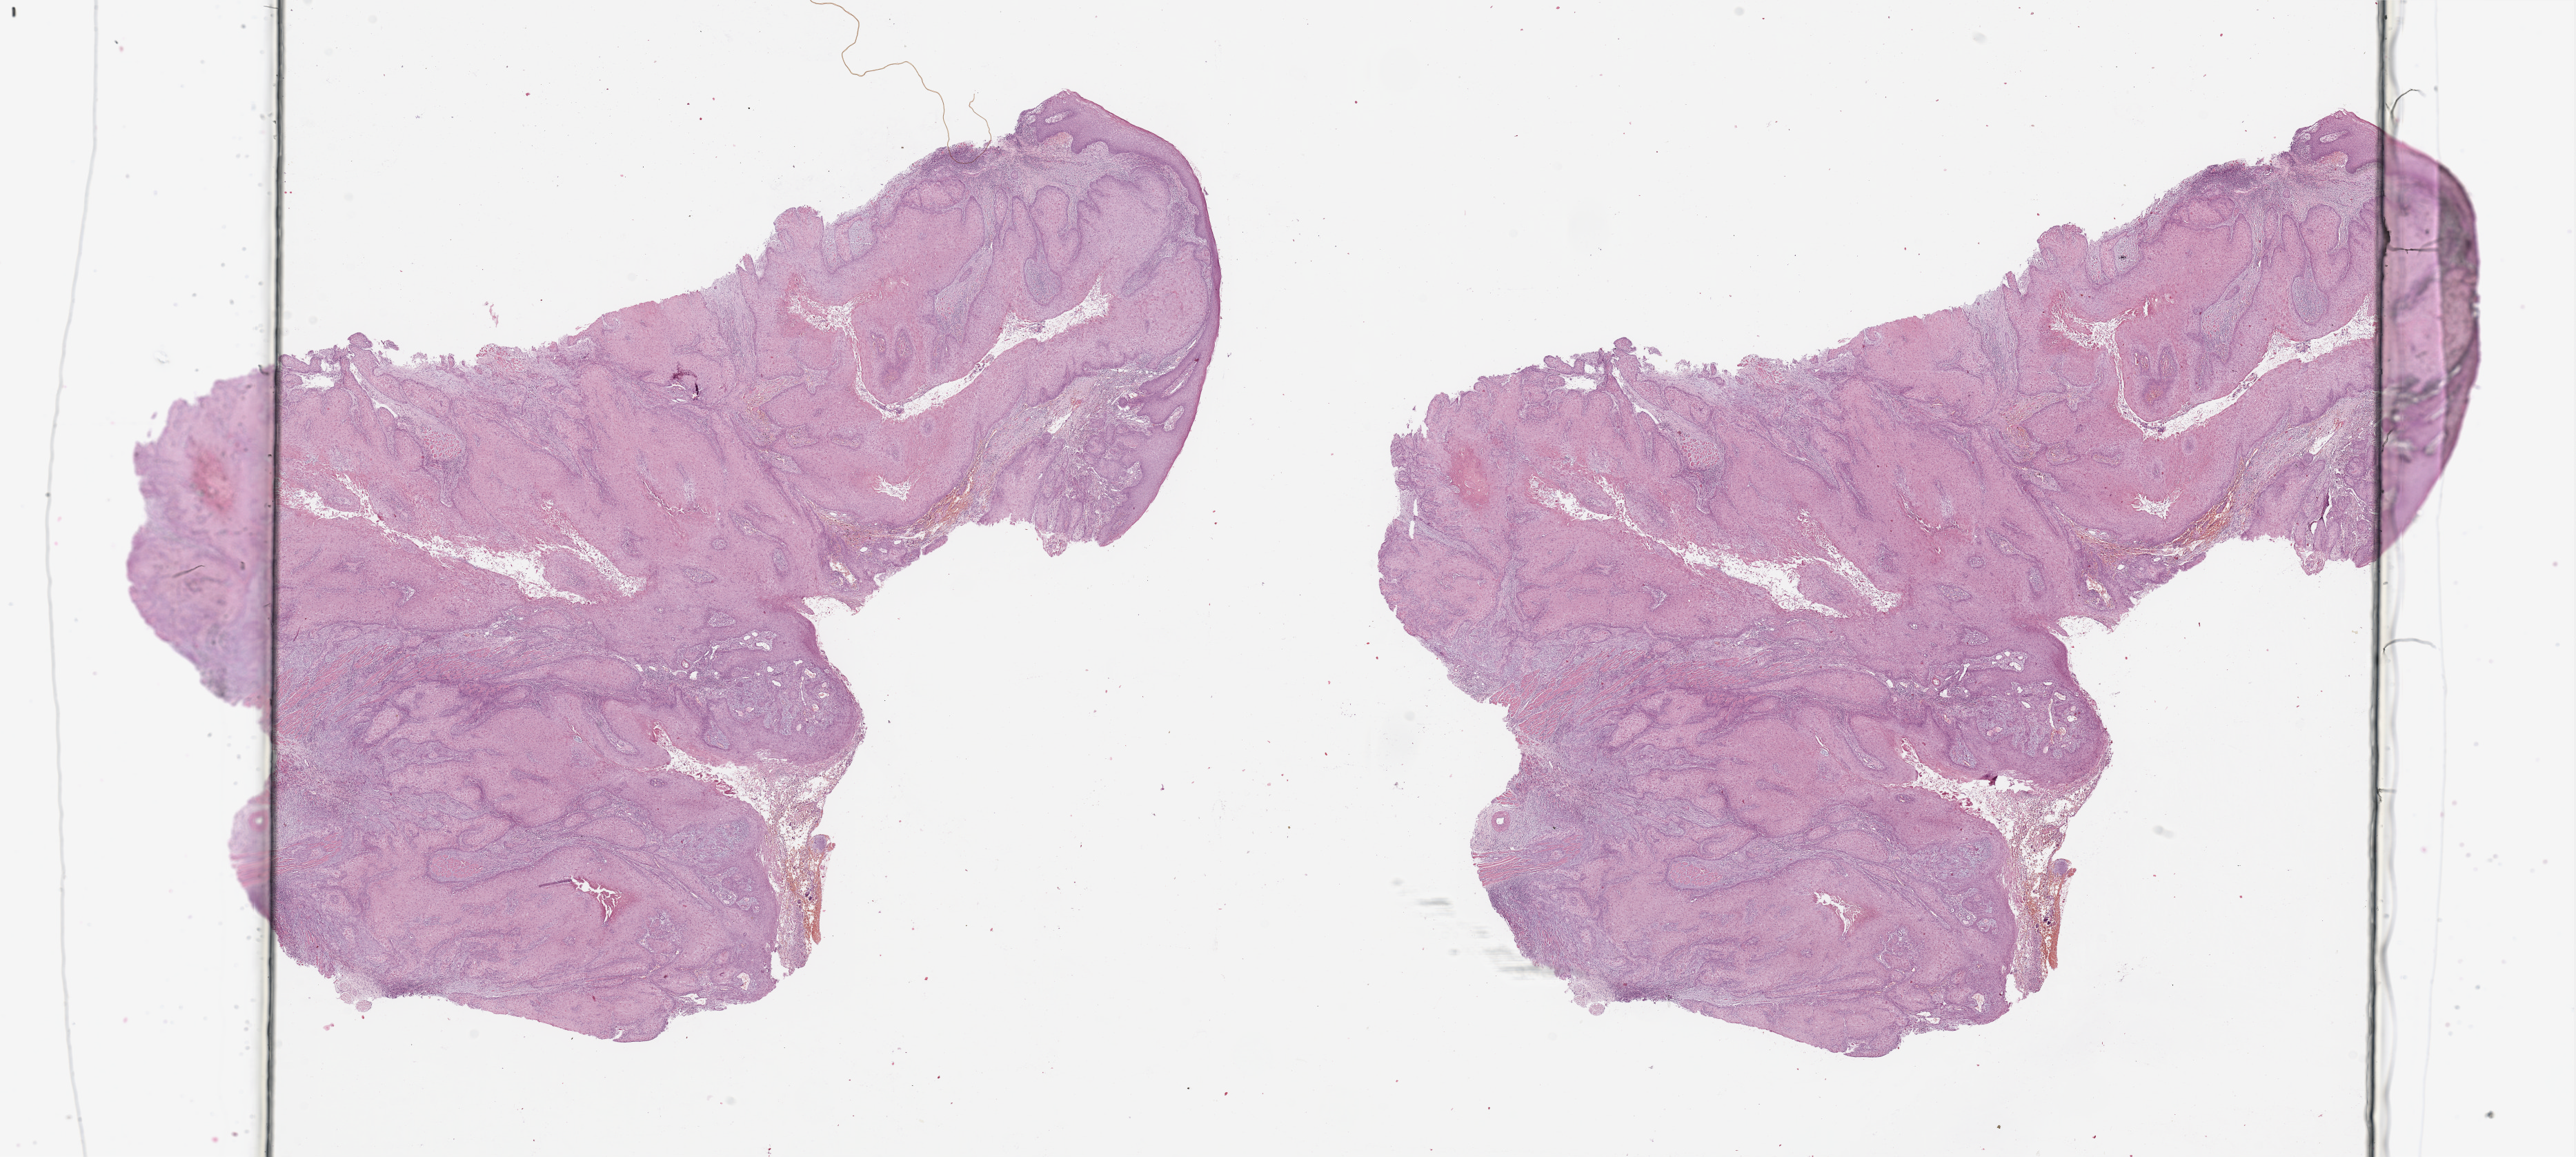
H&E-stained whole-slide image, shown as a low-resolution overview of the whole scanned area (about 29.5 x 13.3 mm, from a 20x scan), tumour tissue sample, sampled site: tongue. Patient: male, age 54 years.
Histologic diagnosis: Squamous cell carcinoma, NOS.